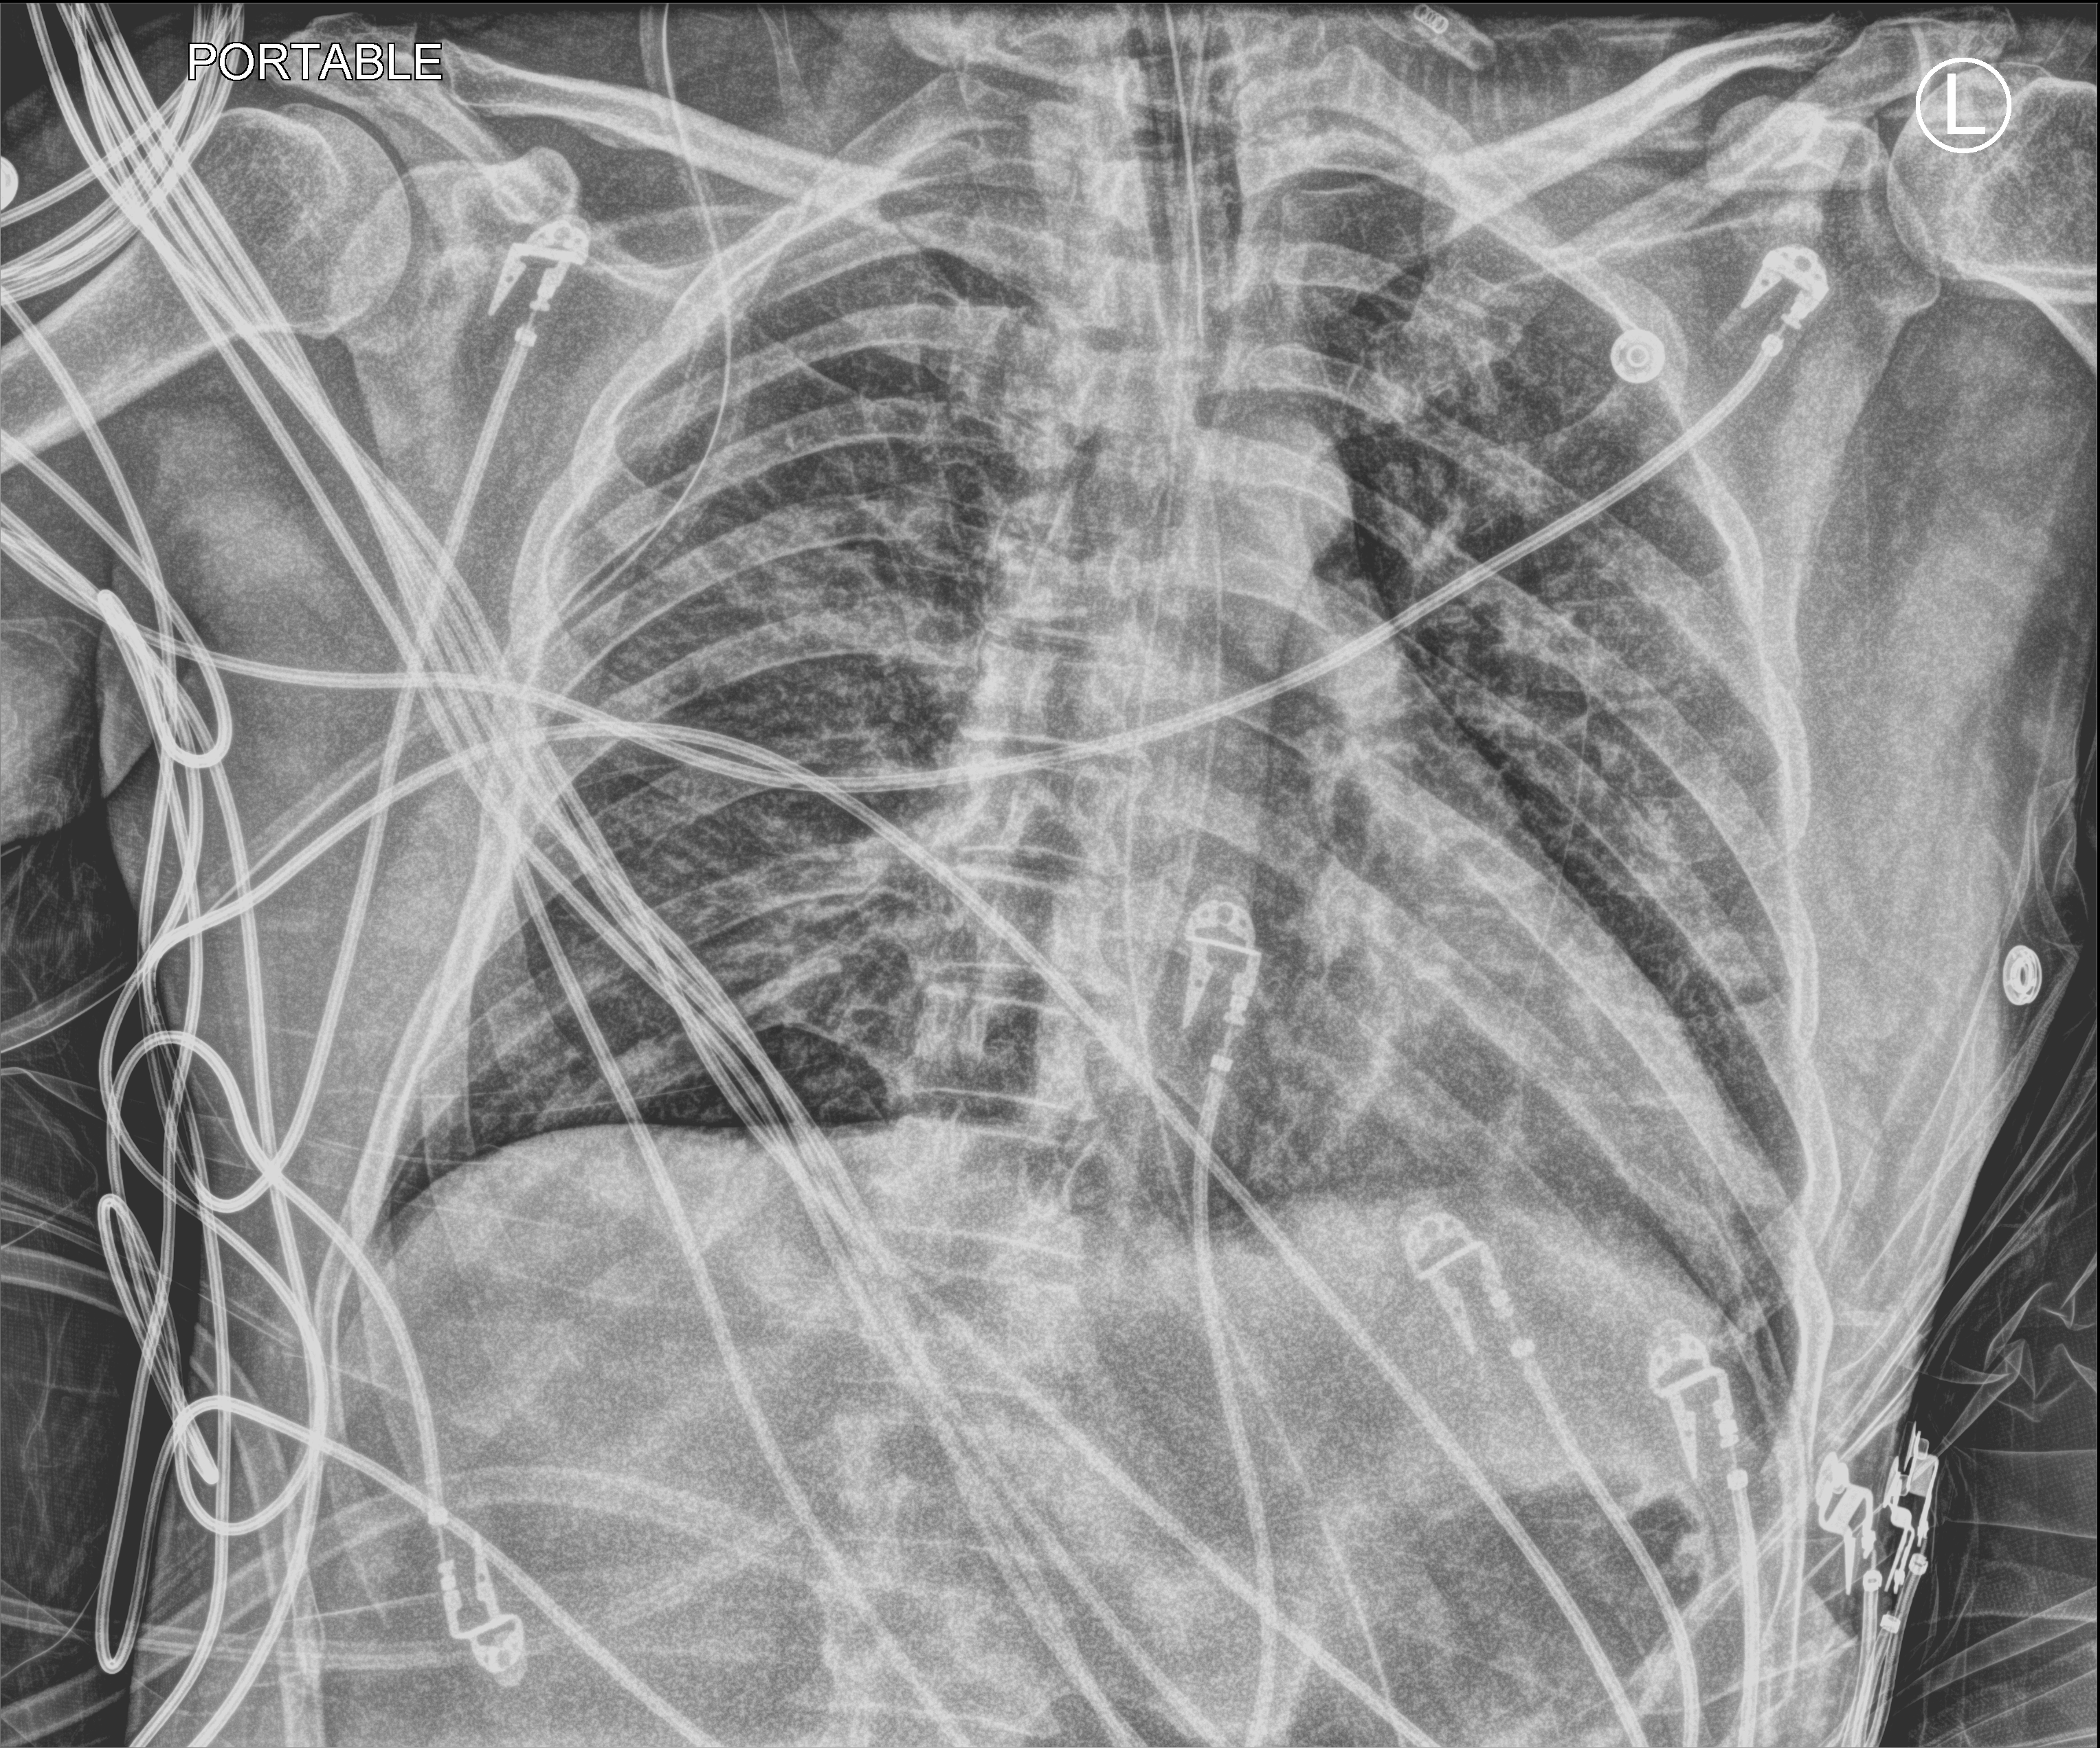
Portable chest radiograph; anteroposterior (AP) projection. Male patient hospitalised with COVID-19, age 18–59 years.
Hospital-stay facts (about this admission, not read from this image; timing relative to this image not recorded):
- mechanically ventilated during this hospital stay: yes
- admitted to intensive care during this hospital stay: yes
- length of hospital stay: 14 days